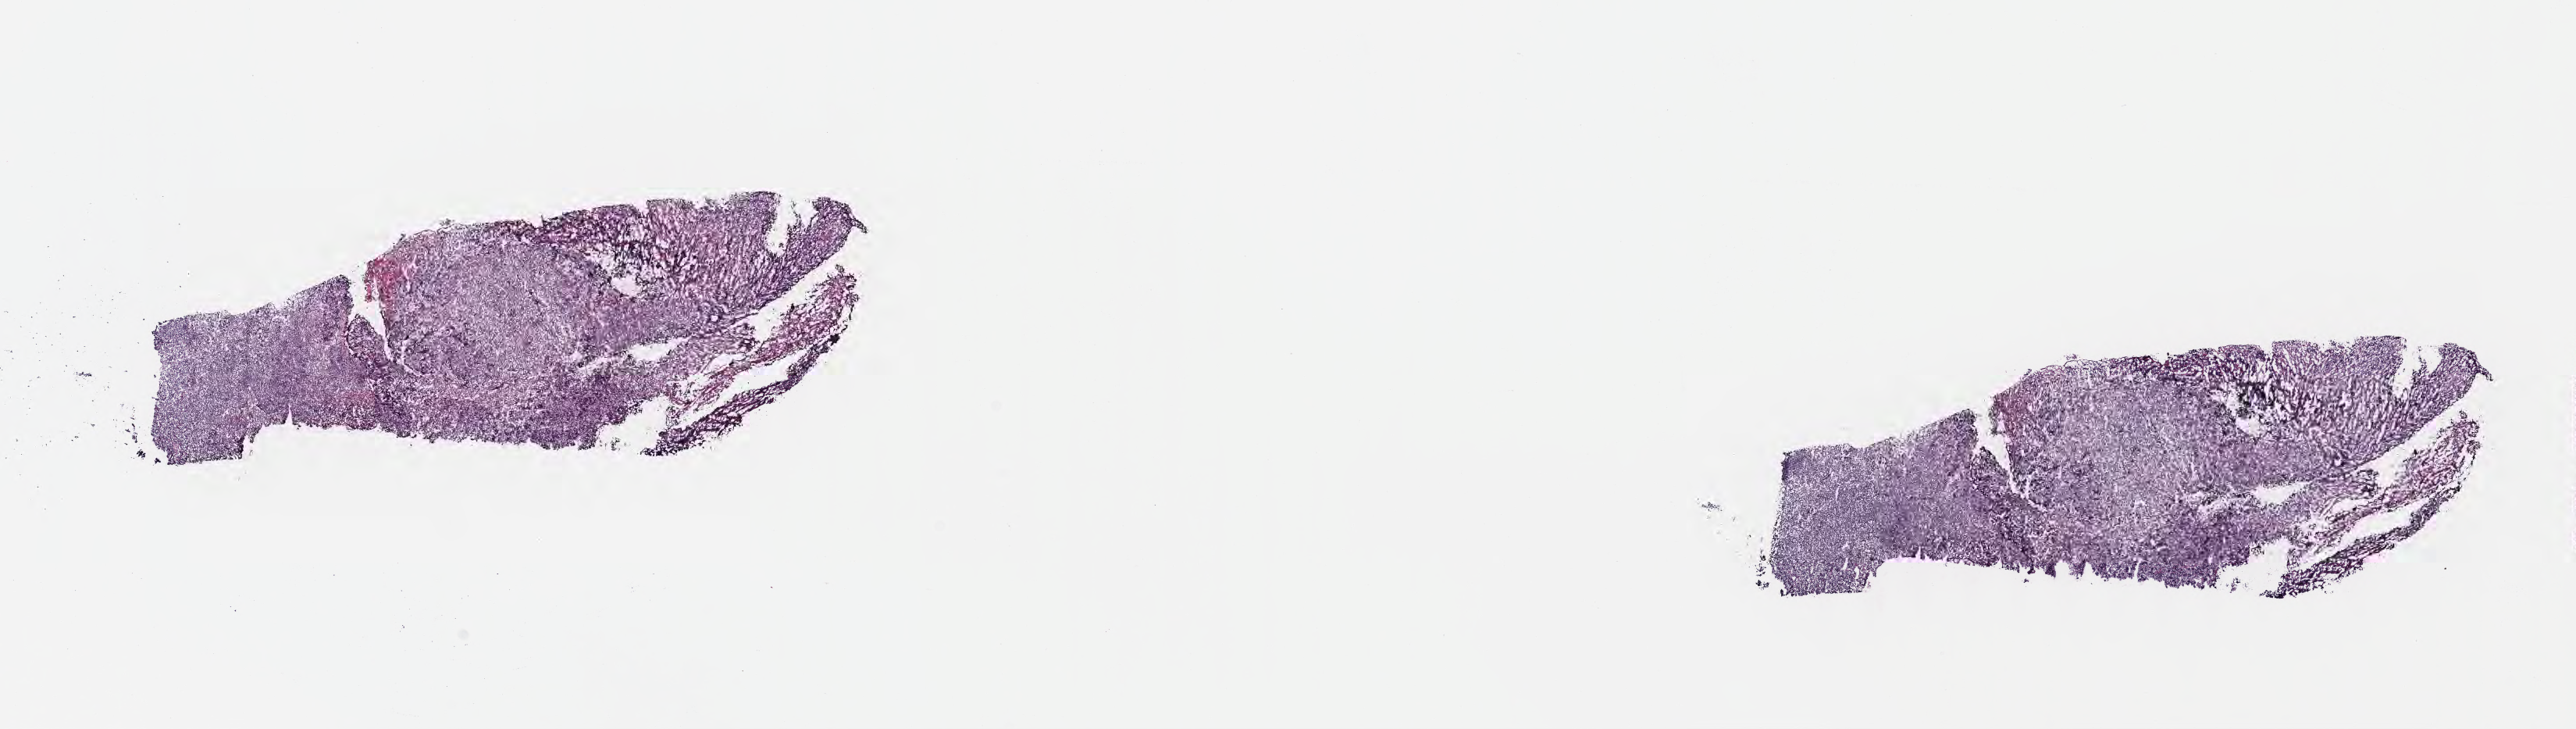
H&E whole-slide image — low-resolution overview of the scanned area, about 26.7 x 7.5 mm. Cryosection. Specimen: primary tumor. Site: lymph node of head and neck. Male patient; age at initial diagnosis 5 years. Slide review estimates, as recorded: tumor cells 90%, tumor nuclei 95%, stromal cells 5%, necrosis 5%, normal cells 0%. Inflammatory infiltration, as recorded: lymphocyte infiltration 50%, monocyte infiltration 30%, neutrophil infiltration 5%.
* Ann Arbor stage (patient): Stage III
* diagnosis: Burkitt lymphoma, NOS